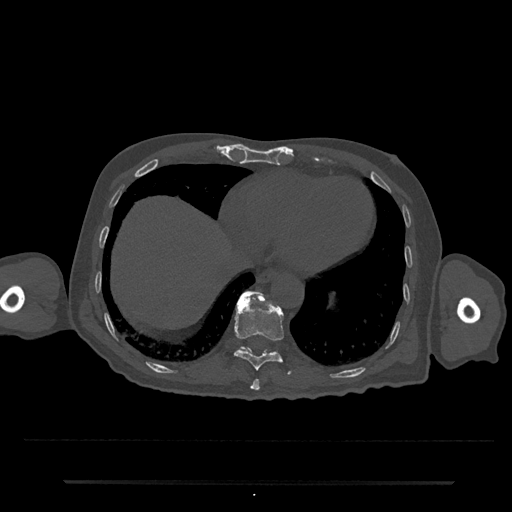
CT including the spine, one axial slice; position 305 of 797 along the scan axis; reconstruction kernel Br40s/3; 120 kVp; bone window (W 1800 / L 400 HU); 0.5 mm slice thickness; 512 × 512 image matrix, field of view 427 × 427 mm. Patient: male, 74 years. From the clinical record (not read from this slice): primary cancer: prostate.
Structures marked on this image (semi-automatically segmented with operator editing):
- T10 vertebra: bounding box <234,293,291,375> (left, top, right, bottom; pixels)
- T11 vertebra: <239,291,263,351>
- T9 vertebra: <250,379,260,391>